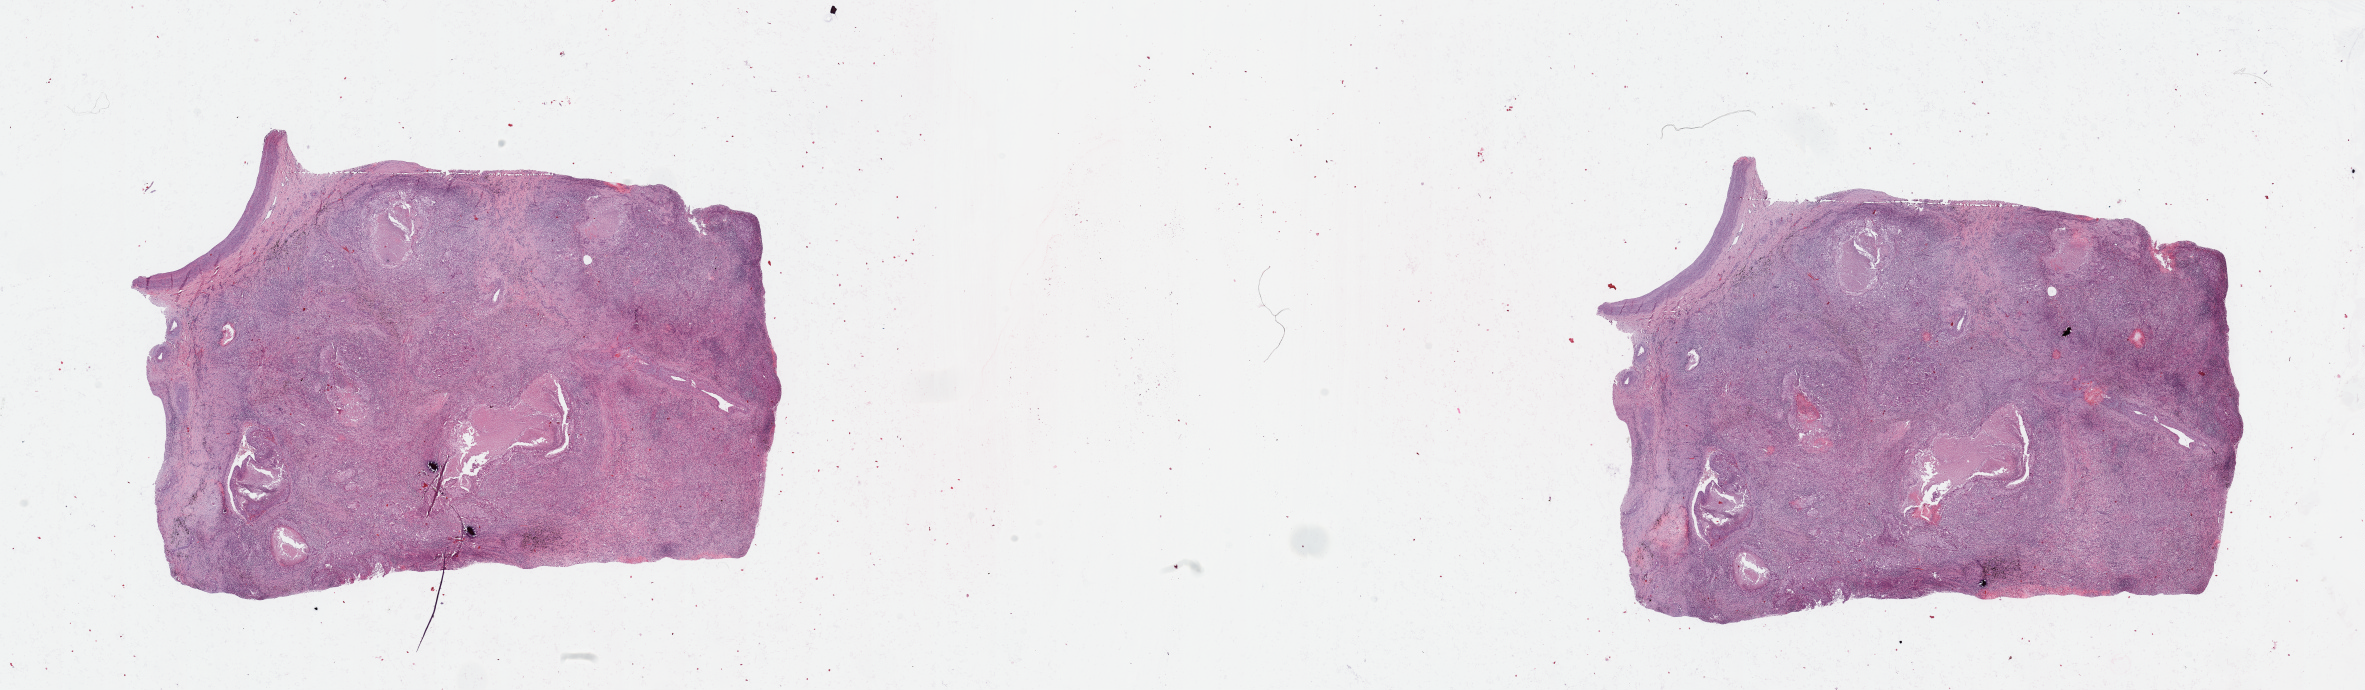
Whole-slide histology image, Hematoxylin and eosin (H&E) stained, whole scanned area (about 37.4 x 10.9 mm, from a 20x scan) shown as a low-resolution overview; lung, tumour tissue. 57-year-old male patient. Histologic grade: G2 (moderately differentiated).
Primary tumour site (as recorded): right lower lobe. AJCC pathologic stage: IIB. Diagnosis: Squamous cell carcinoma, NOS.